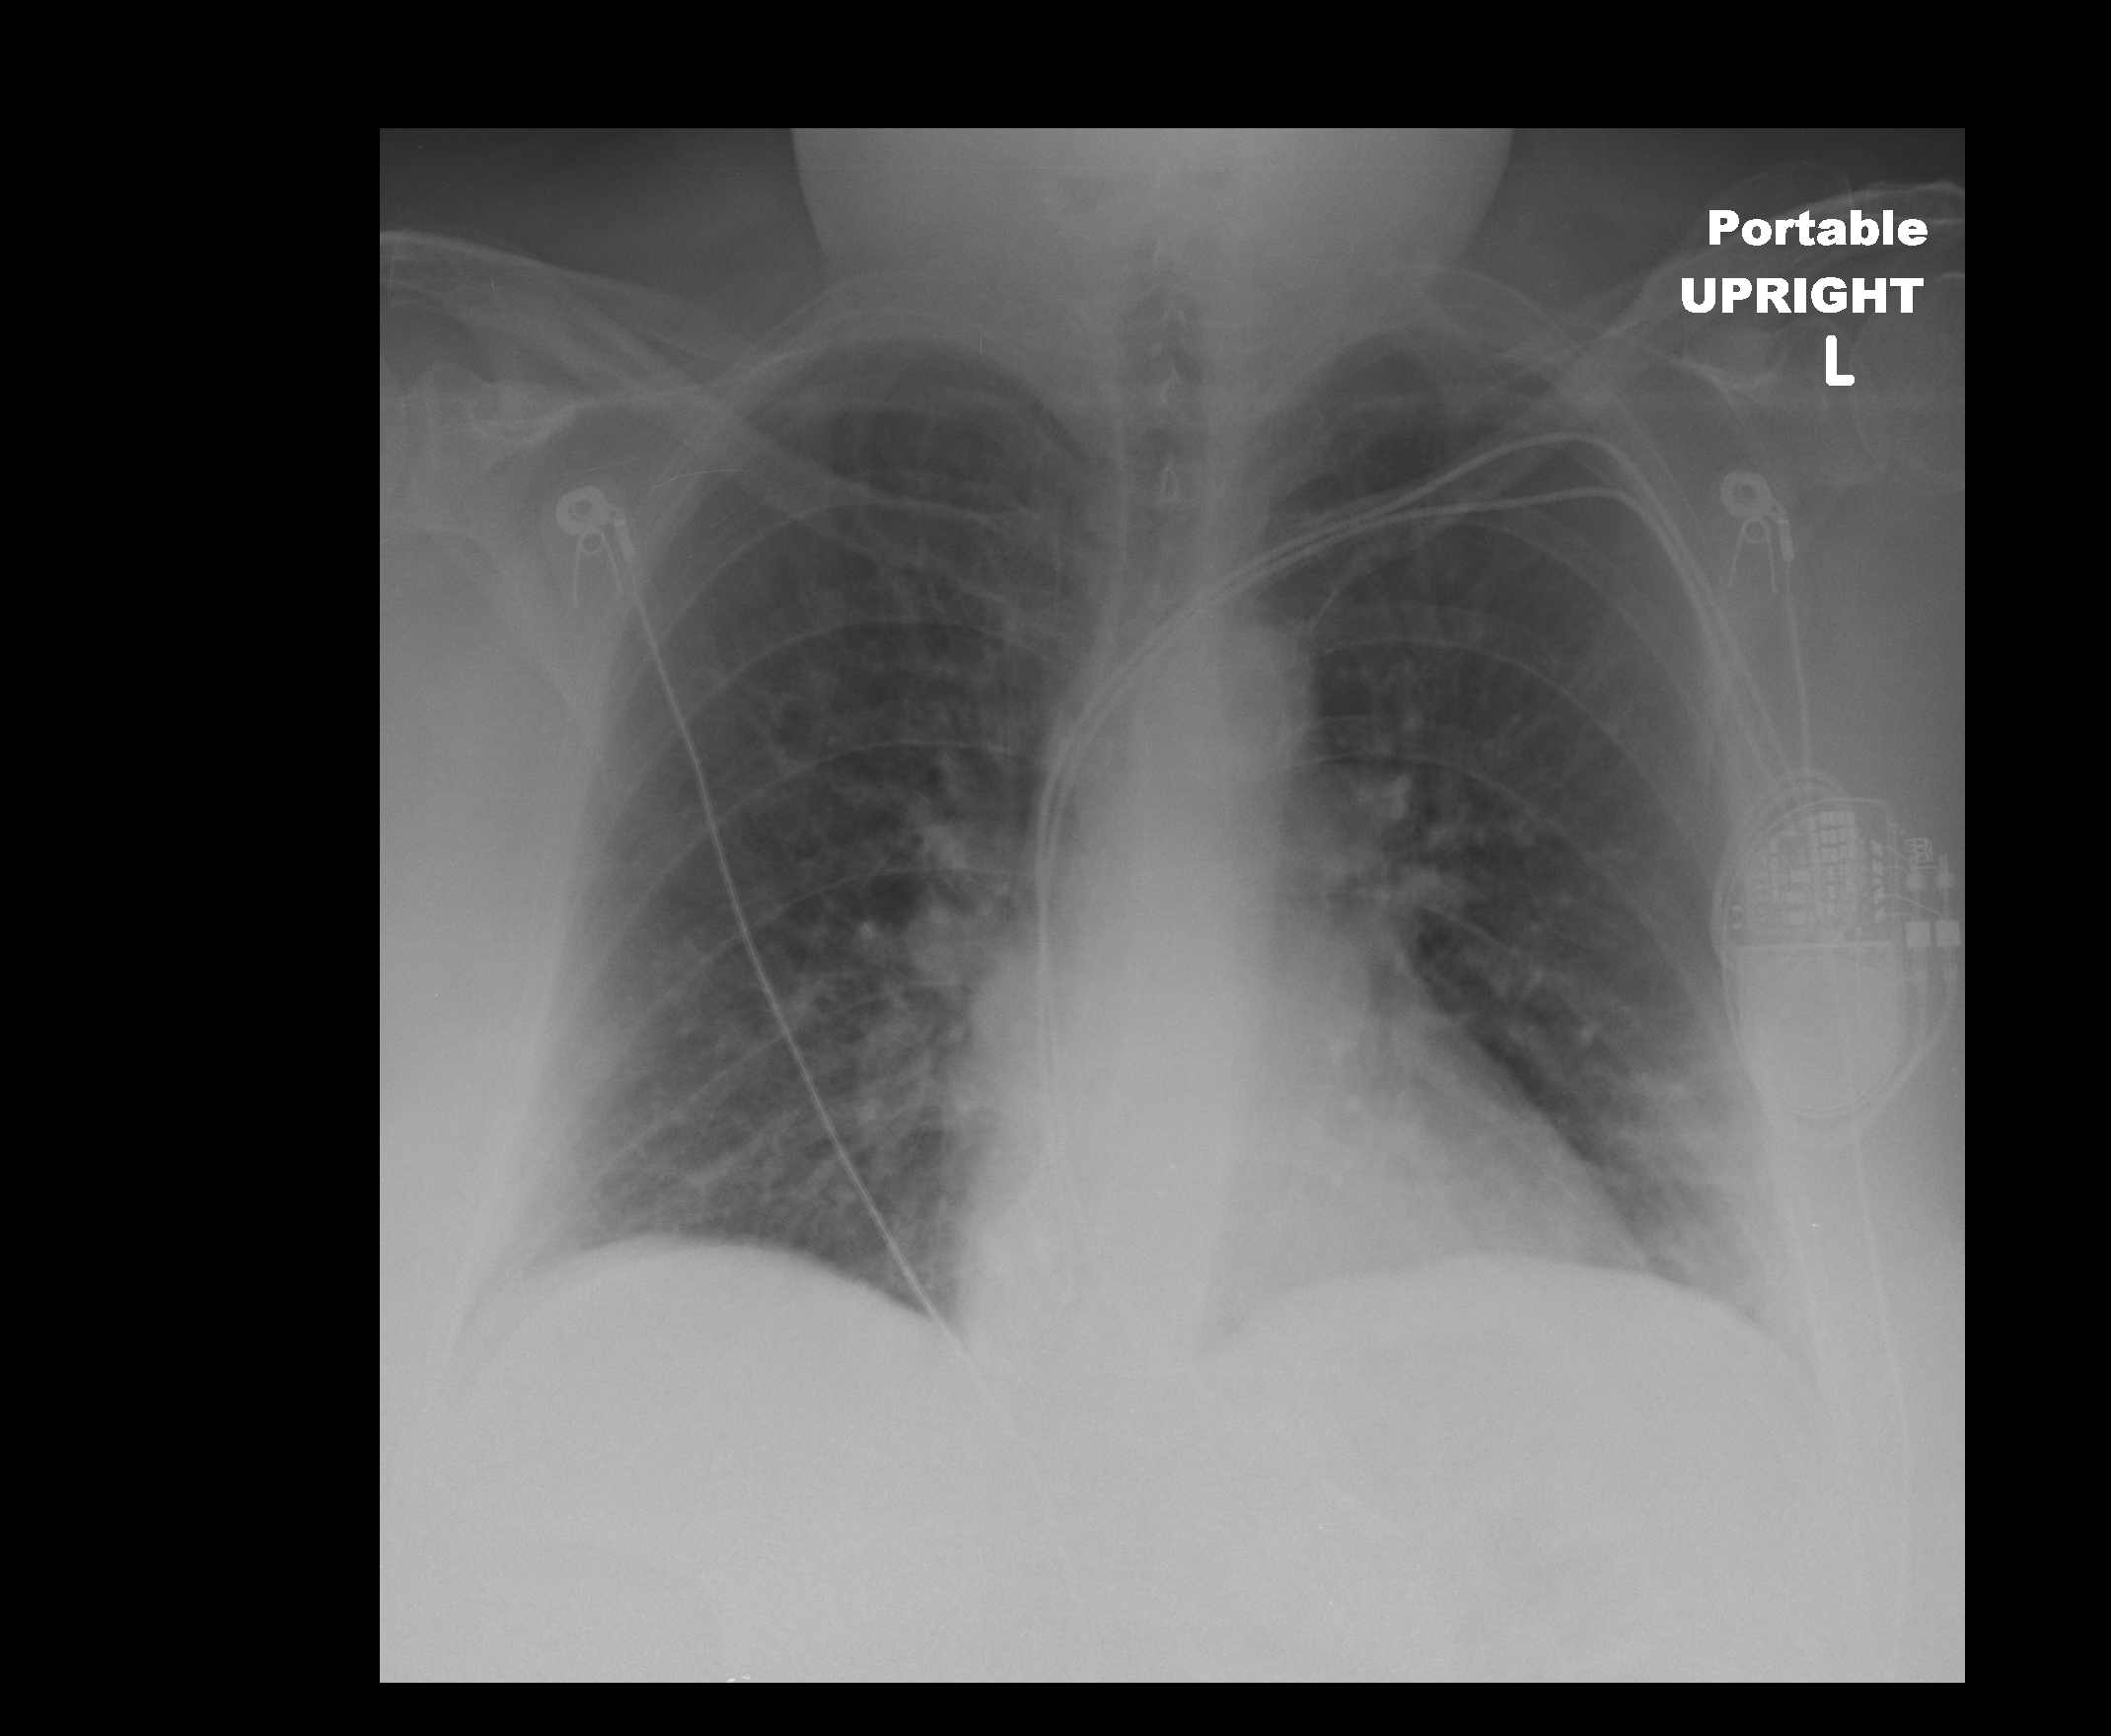
Portable chest radiograph, AP projection. Female patient, age 57 years; COVID-19 (test-positive).
Radiologist's key findings for this exam: Increased interstitial changes in both lungs are symmetric.